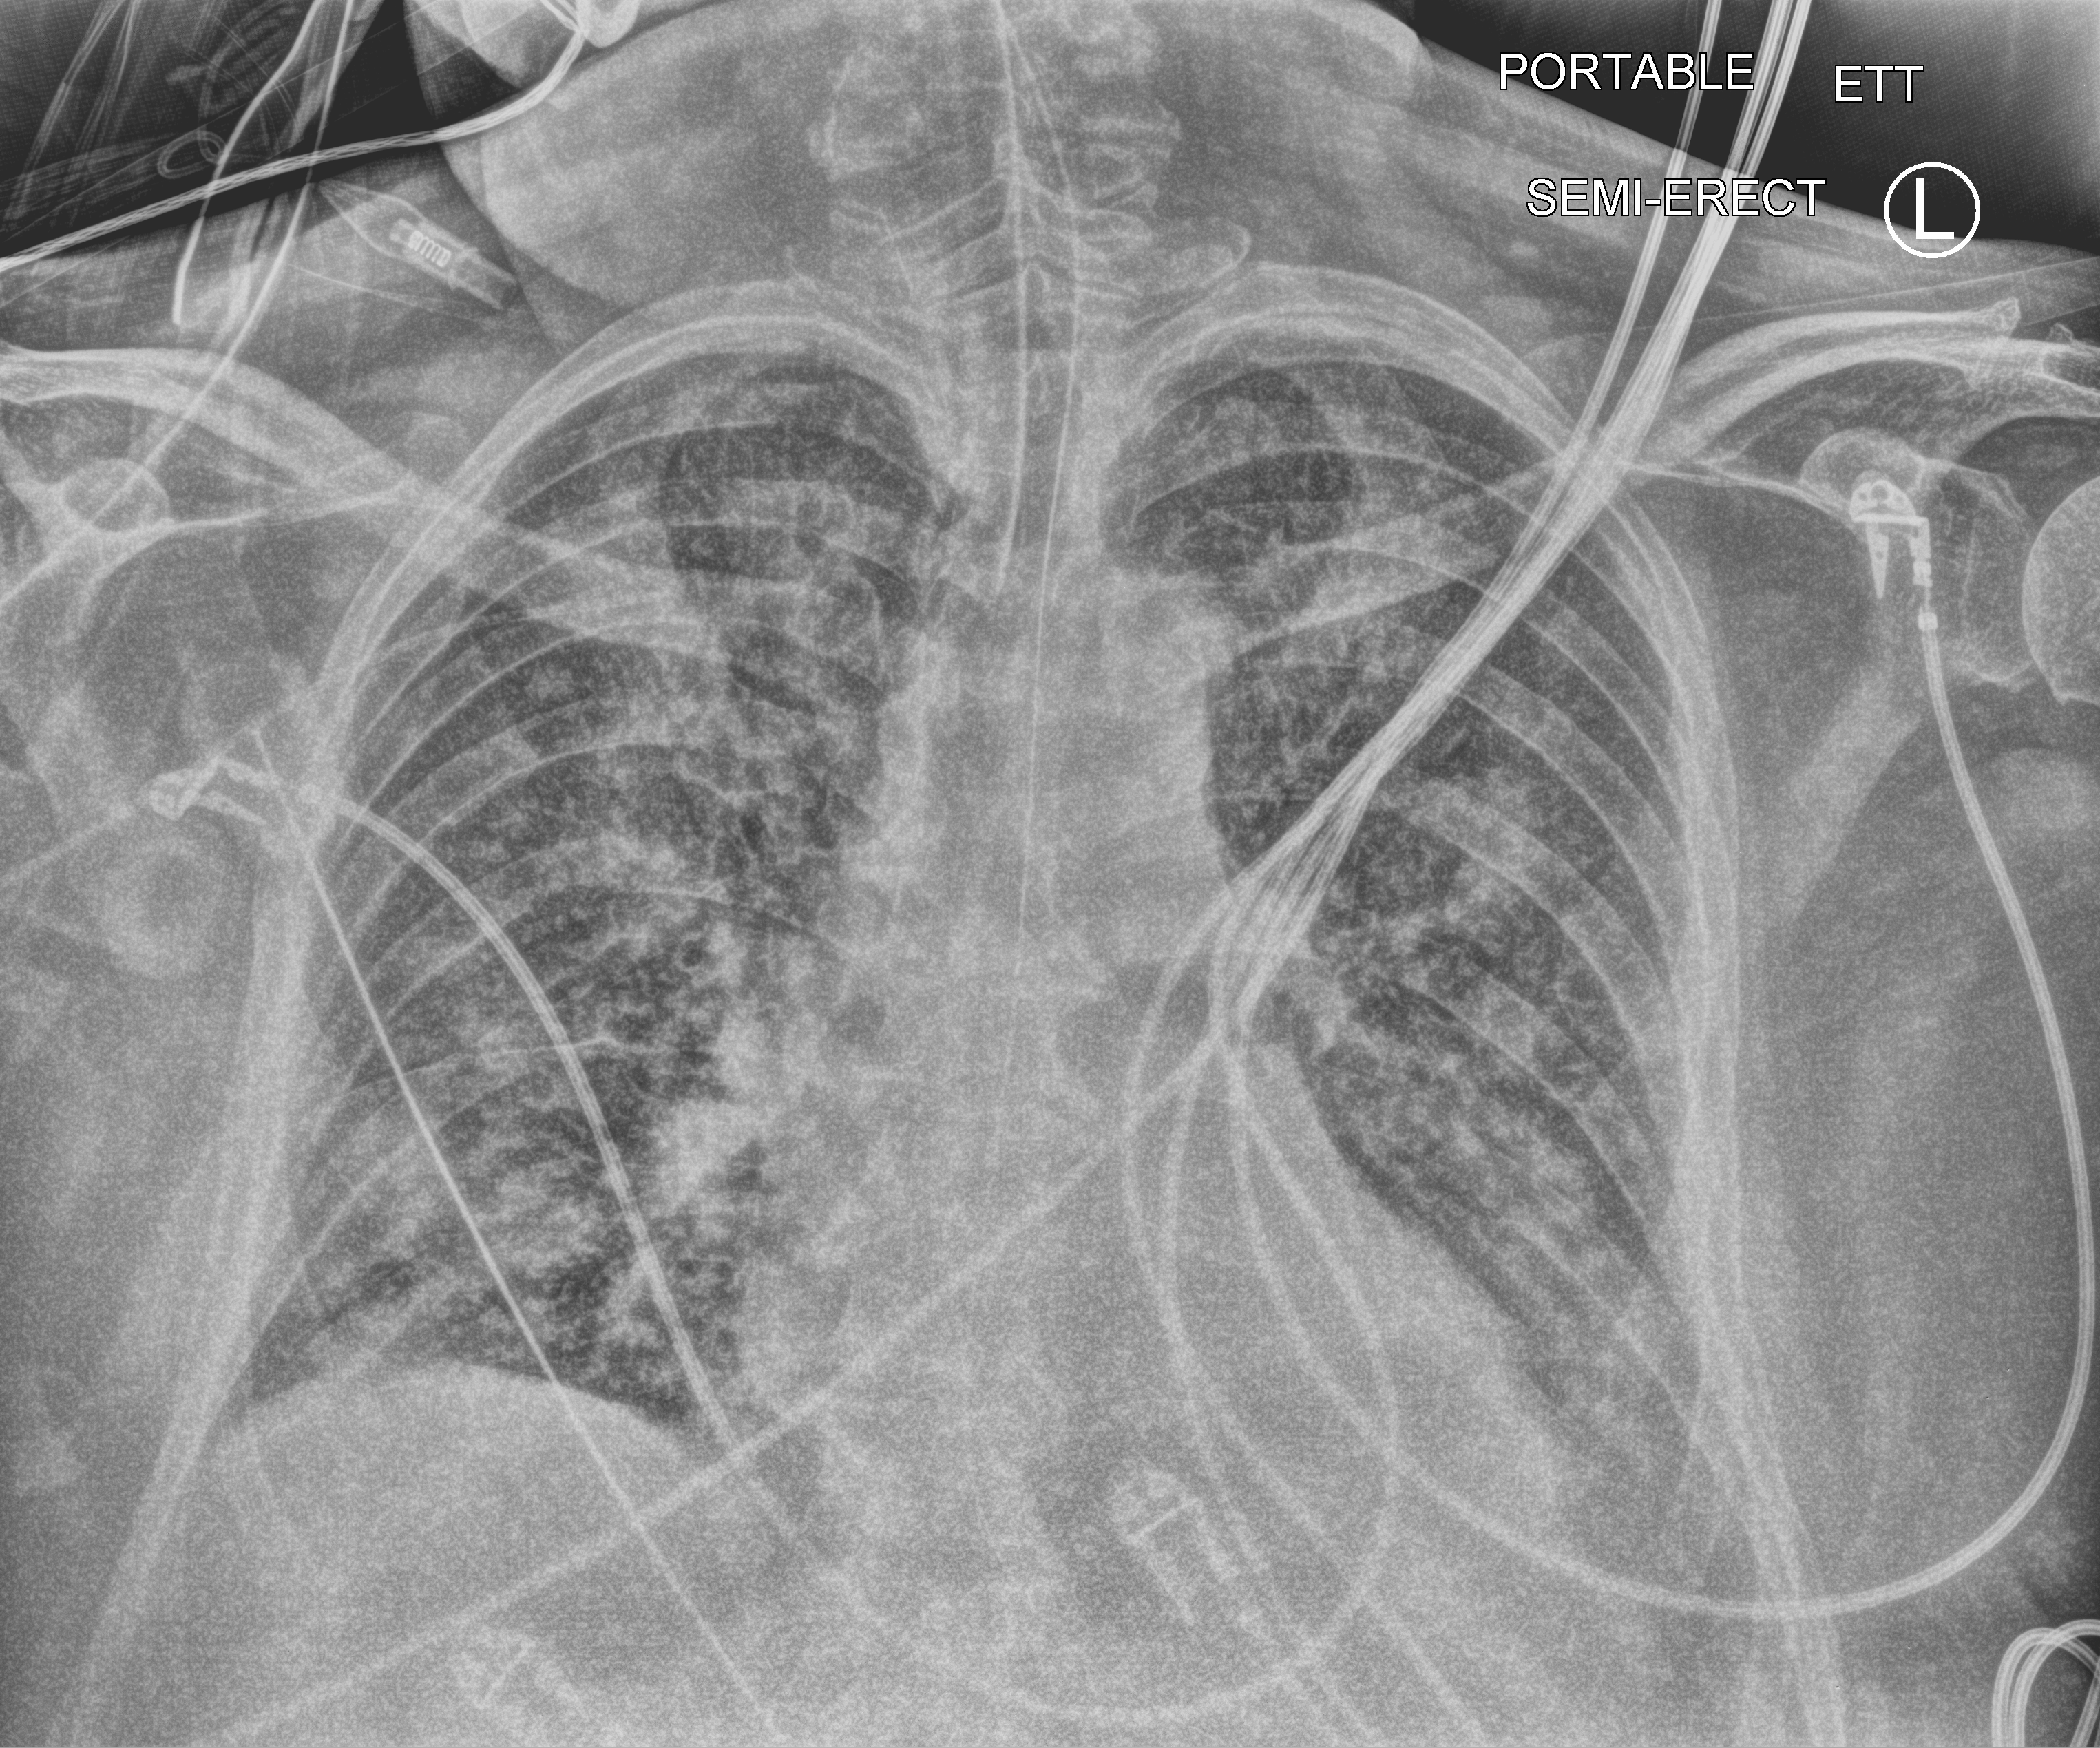
Chest X-ray (portable), anteroposterior (AP) projection. Patient hospitalised with COVID-19; male, aged 60–74 years.
From the hospital-stay record, not from the radiograph (when in the stay this image was taken is not recorded):
- mechanically ventilated during this hospital stay: yes
- admitted to intensive care during this hospital stay: yes